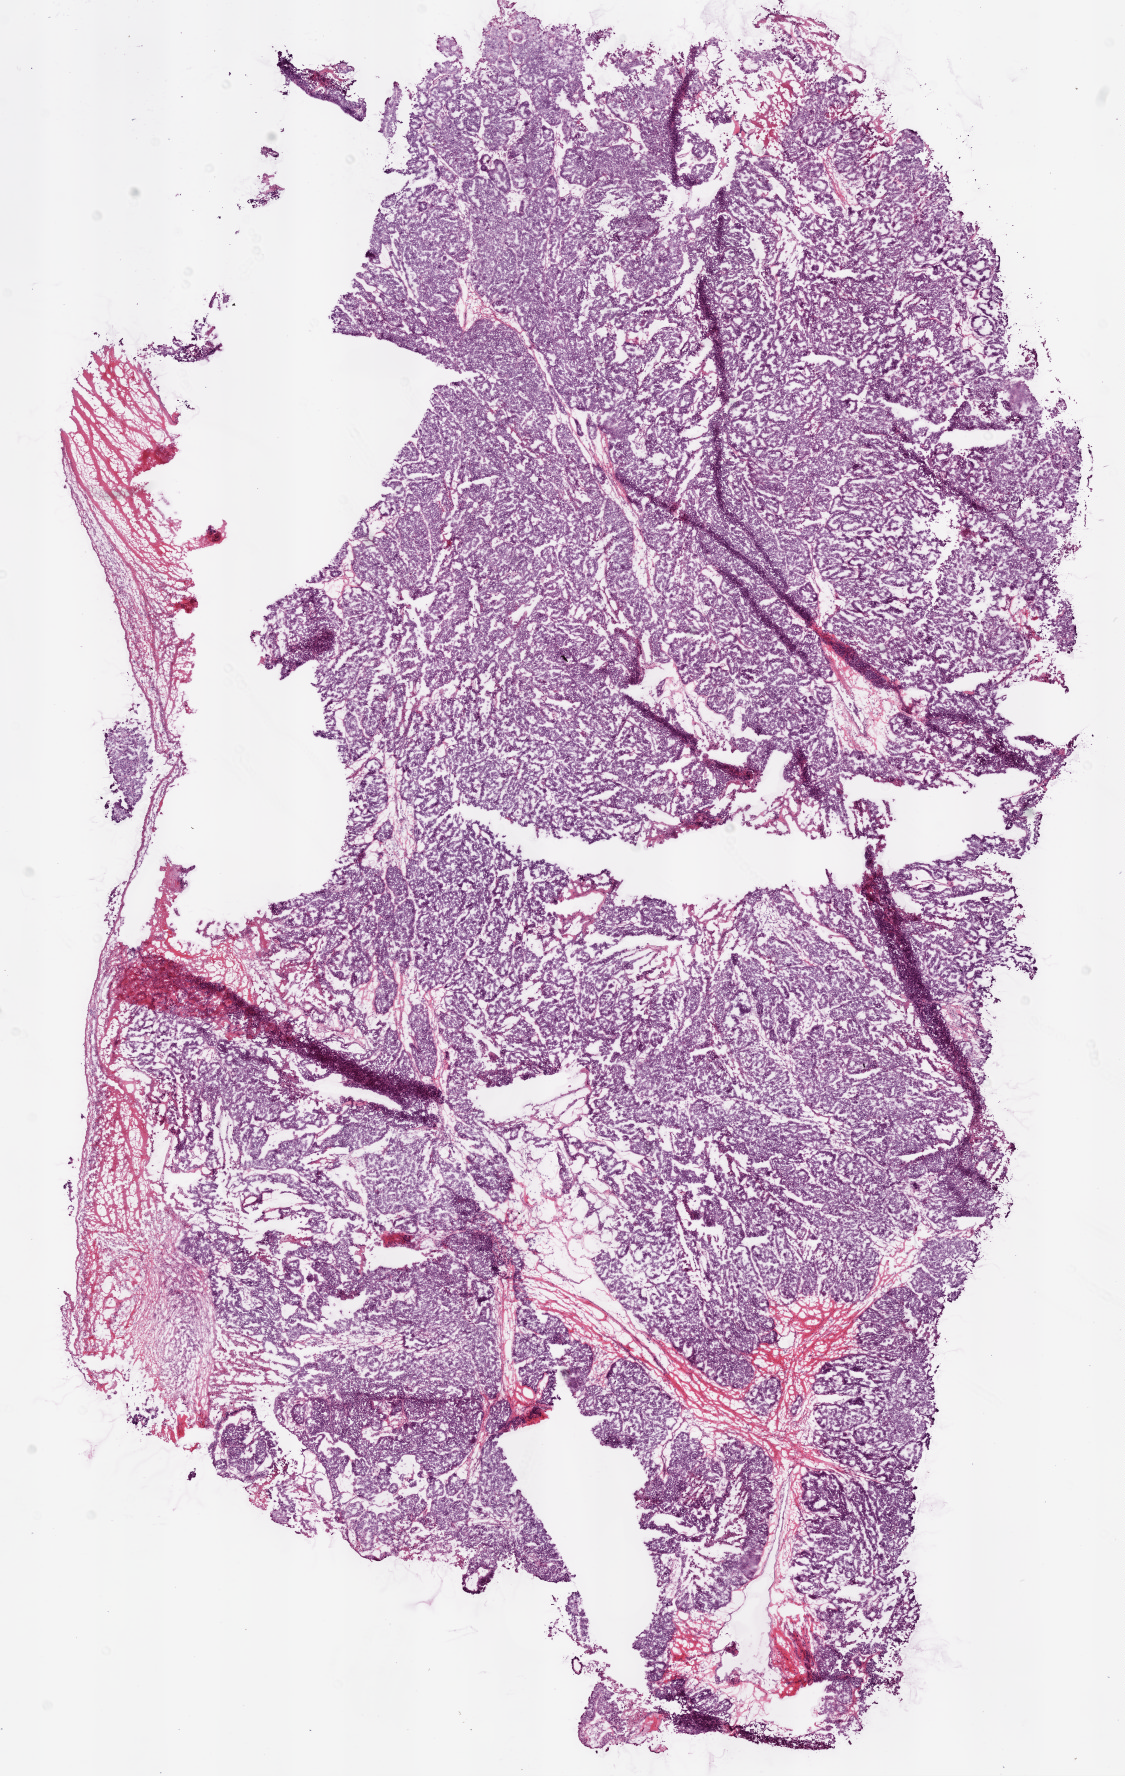
Whole-slide histology image, H&E — whole scanned area (about 9.0 x 14.3 mm, slide scanned at 20x) shown as a low-resolution overview. Frozen section from the bottom of the tissue portion. Primary tumour sample from the ovary. Female patient; age at initial diagnosis 45 years. Histologic grade: G3 (poorly differentiated). Slide review estimates, as recorded: tumour cells 98%, tumour nuclei 99%, normal cells 0%, stromal cells 1%, necrosis 1%.
Histologic diagnosis: Serous cystadenocarcinoma, NOS. FIGO stage: IIIC.